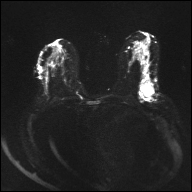
Breast MRI, one axial slice; slice 16 of 32 in the series (ordered by position); diffusion-weighted series; image 2 of 4 stored at this slice position (different b-values; order by instance number); 1.5 T; 4 mm slice thickness; 192 × 192 image matrix. Female patient.
Annotated regions visible in this slice (outlined manually by an expert reader):
- tumour on diffusion-weighted imaging: bounding box (x1, y1, x2, y2) in pixels: (141, 81, 154, 97)